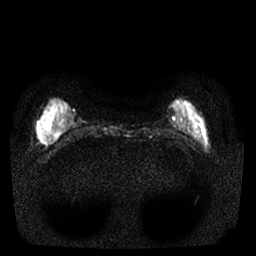
Breast MRI, one axial slice; slice 2 of 25 in the series (ordered by position); diffusion-weighted series; image 2 of 4 stored at this slice position (different b-values; order by instance number); 1.5 T; 4 mm slice thickness; 256 × 256 image matrix. Female patient.
Structures marked on this image (manually delineated by an expert):
- tumour on diffusion-weighted imaging: bounding box <54,130,61,138> (left, top, right, bottom; pixels)